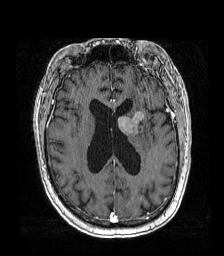
Brain MRI from a brain-tumour surgery series, one axial slice; position 70 of 192 along the scan axis; T1-weighted post-contrast; 1 mm slice thickness; 224 × 256 image matrix, field of view 219 × 250 mm. Case-level facts recorded for this patient, not image findings: histopathology: Metastatic carcinoma from lung primary; tumour location: Left Frontal Caudate.
Structures marked on this image (manually delineated by an expert):
- tumour: bounding box <117,110,148,145> (left, top, right, bottom; pixels)